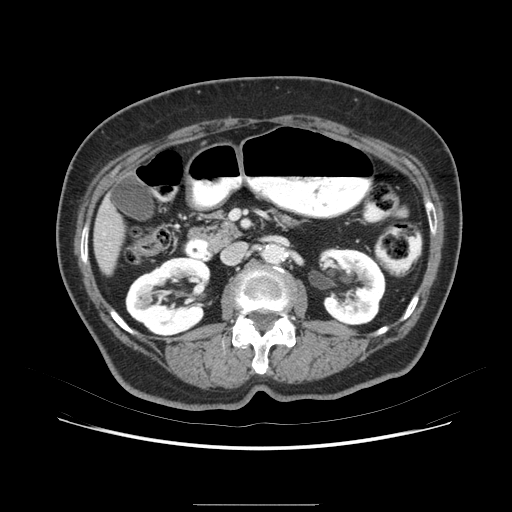
Contrast-enhanced abdominal CT (liver protocol), one axial slice. Position 25 of 79 along the scan axis. 120 kVp. Soft-tissue window (W 400 / L 40 HU). 512 × 512 image matrix. Case-level facts recorded for this patient, not image findings: diagnosis: hepatocellular carcinoma (patient treated with transarterial chemoembolisation; whether this scan precedes or follows treatment is not stated here); TNM stage (as recorded): Stage-I; Child-Pugh class: A; tumour differentiation: poorly differentiated.
Structures marked on this image (semi-automatically segmented with operator editing):
- liver parenchyma outside the tumour (the mass and vessels are separate outlines, so this box may not span the whole liver): box from (x=92, y=134) to (x=252, y=292) px
- liver vessels: (x=116, y=223)–(x=122, y=247)